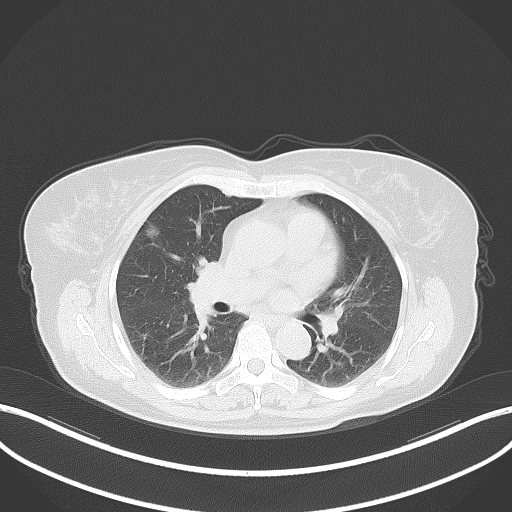
Chest CT, one axial slice. Position 37 of 64 along the scan axis. 120 kVp. Lung window (W 1500 / L -600 HU). 512 × 512 image matrix. Patient: female, 55 years. From the clinical record (not read from this slice): clinical TNM (as recorded): T1b N0 M0.
Outlined on this slice (bounding box drawn by a radiologist):
- lung tumour (recorded histology: adenocarcinoma): box from (x=143, y=223) to (x=162, y=243) px